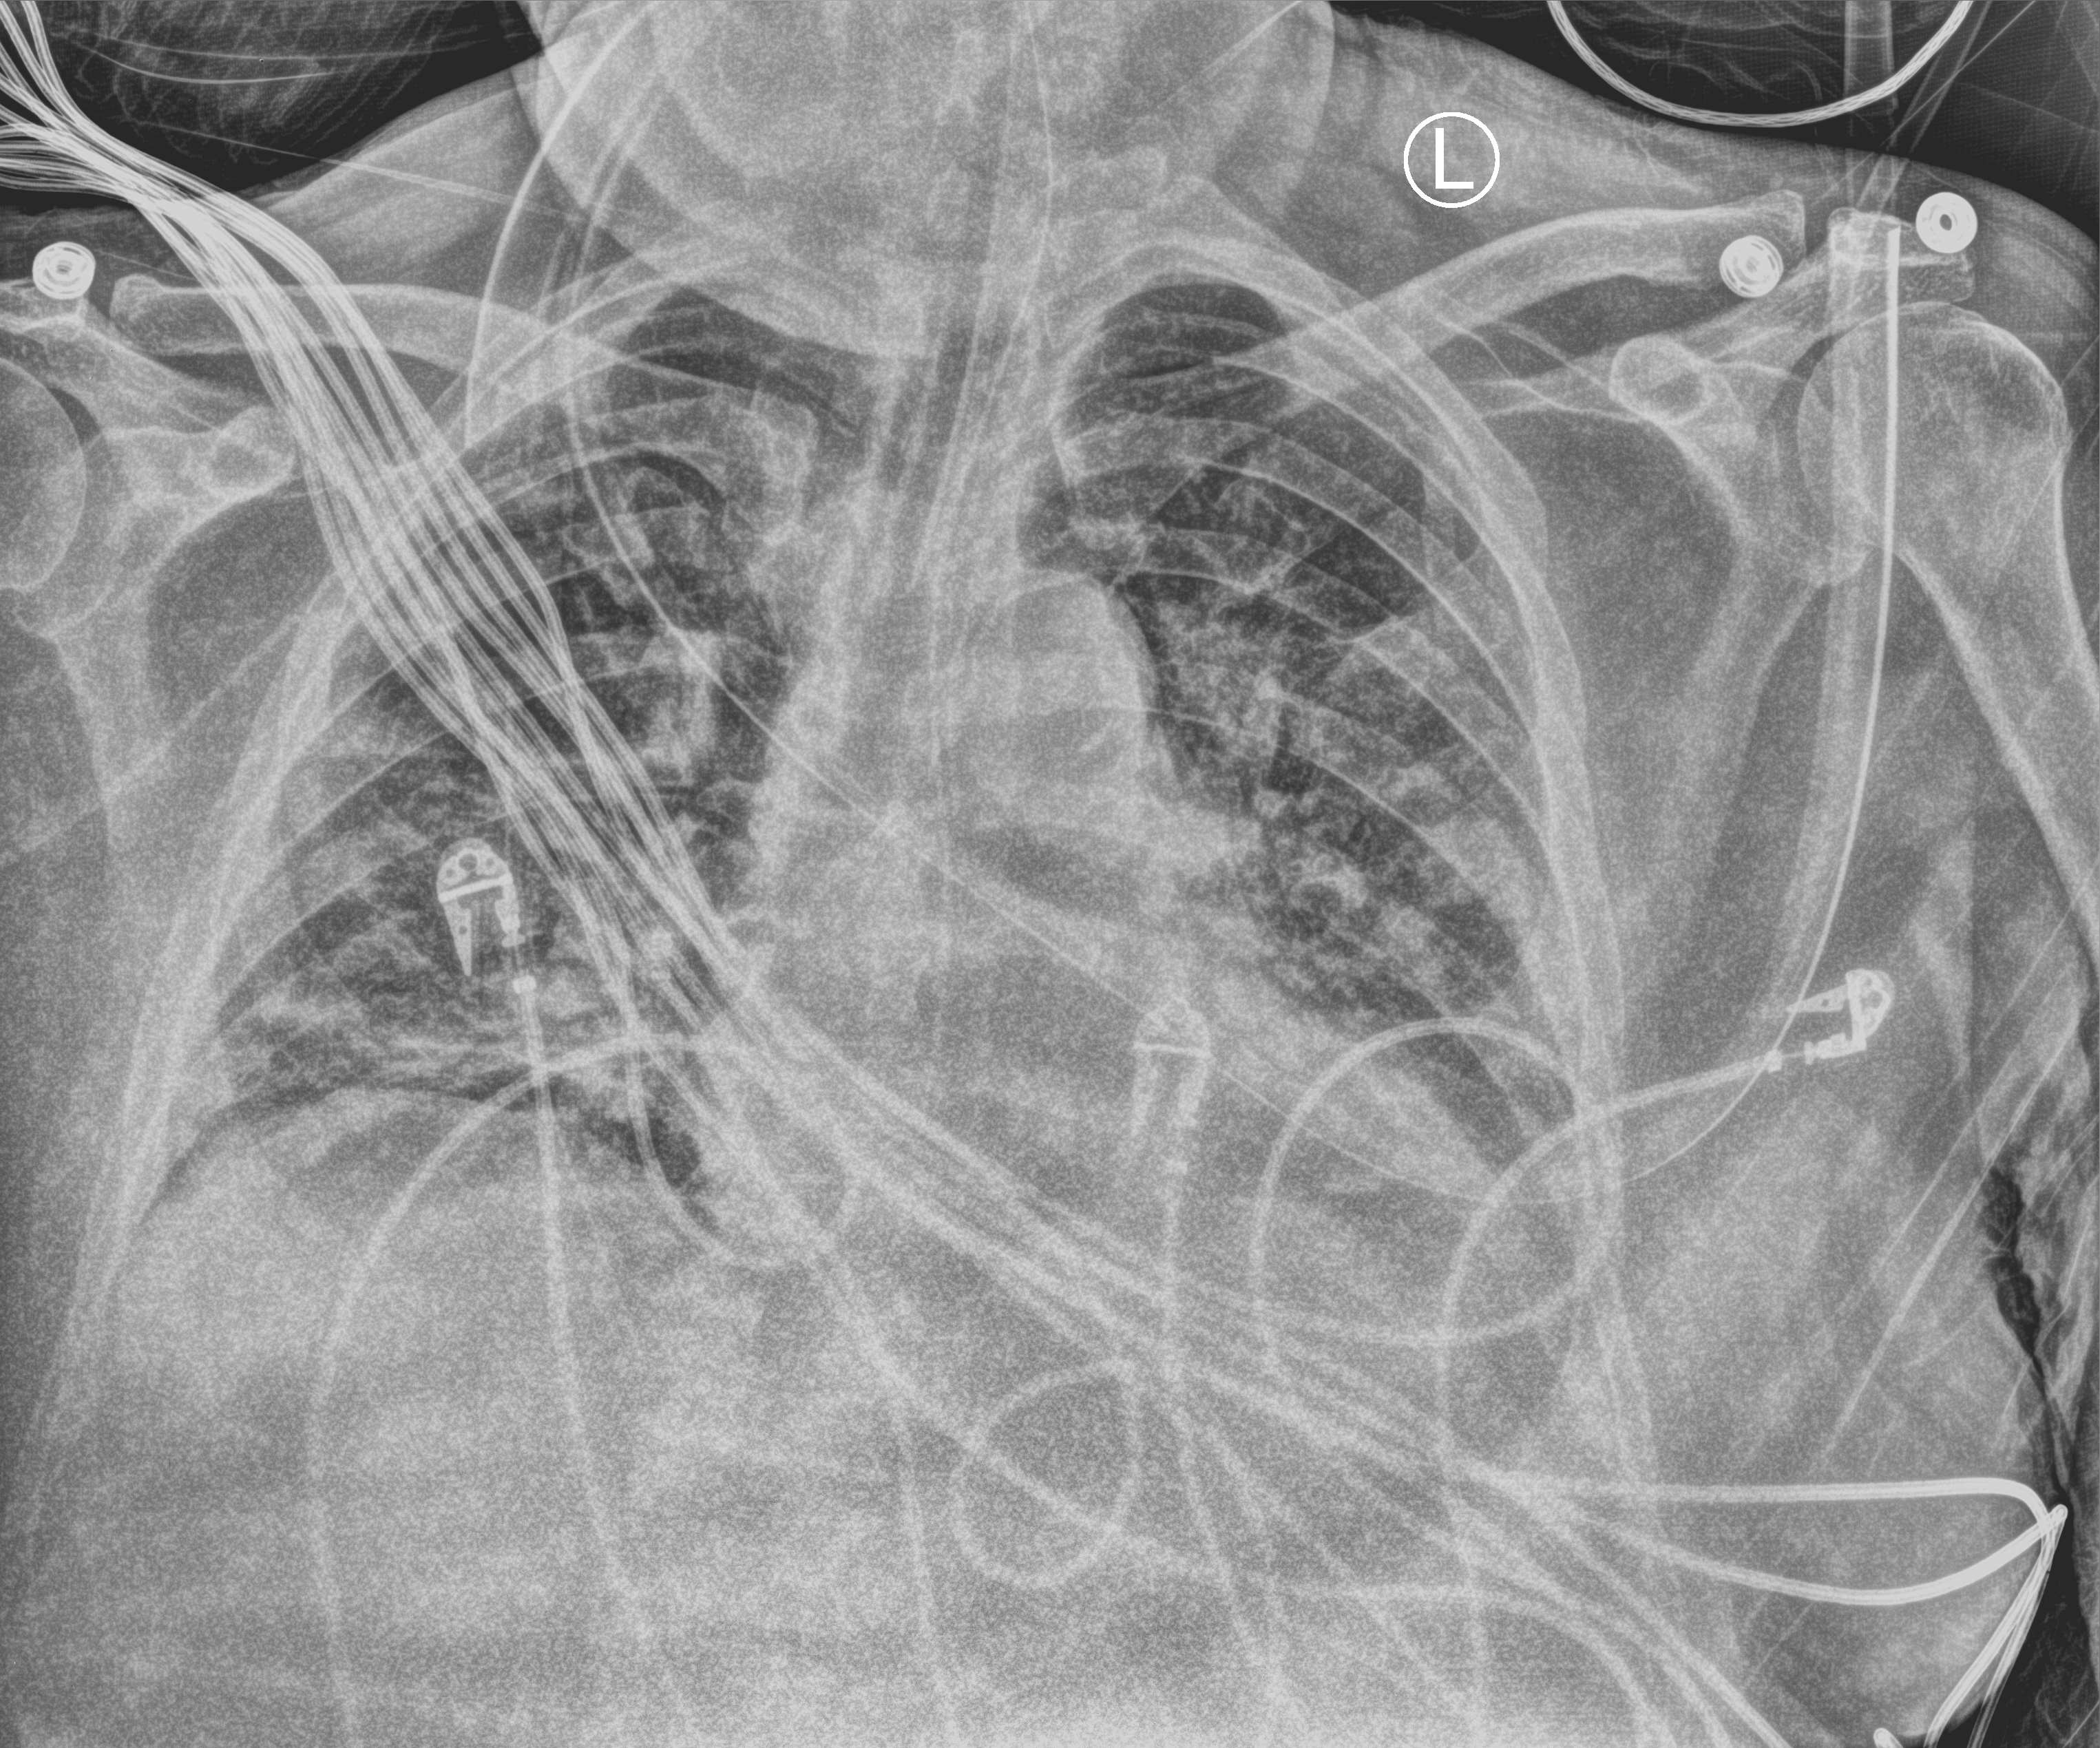
Chest X-ray (portable), anteroposterior (AP) projection. Male patient hospitalised with COVID-19, age 60–74 years.
Hospital-stay facts (about this admission, not read from this image; timing relative to this image not recorded): mechanically ventilated during this hospital stay: yes; admitted to intensive care during this hospital stay: yes.